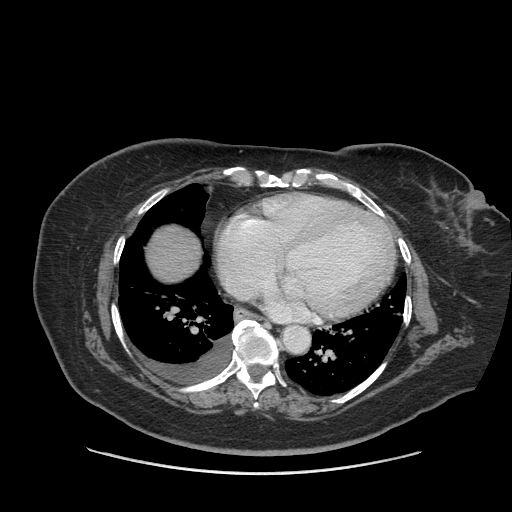
Contrast-enhanced abdominal CT (liver protocol), one axial slice; position 86 of 91 along the scan axis; 140 kVp; soft-tissue window (W 400 / L 40 HU); 2.5 mm slice thickness; 512 × 512 image matrix, field of view 420 × 420 mm. Case-level facts recorded for this patient, not image findings: diagnosis: hepatocellular carcinoma (patient treated with transarterial chemoembolisation; whether this scan precedes or follows treatment is not stated here); TNM stage (as recorded): Stage-I; Child-Pugh class: A; tumour differentiation: well differentiated; tumour nodularity: uninodular.
Outlined on this slice (semi-automatic segmentation, software-assisted and operator-edited):
- liver parenchyma outside the tumour (the mass and vessels are separate outlines, so this box may not span the whole liver): bounding box (x1, y1, x2, y2) in pixels: (146, 224, 200, 282)